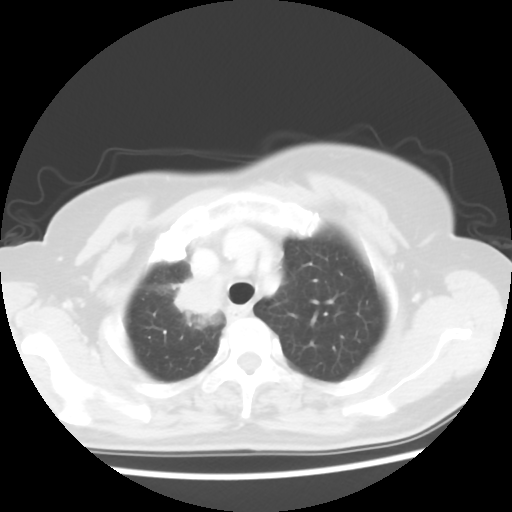
Chest CT, one axial slice. 120 kVp. Lung window (W 1500 / L -600 HU). 5 mm slice thickness. 512 × 512 image matrix, field of view 314 × 314 mm. Female patient, age 62 years. From the clinical record (not read from this slice): clinical TNM (as recorded): T2 N1 M1a.
Outlined on this slice (rectangle marked by the reading radiologist):
- lung tumour (recorded histology: adenocarcinoma): bounding box (x1, y1, x2, y2) in pixels: (167, 276, 222, 330)